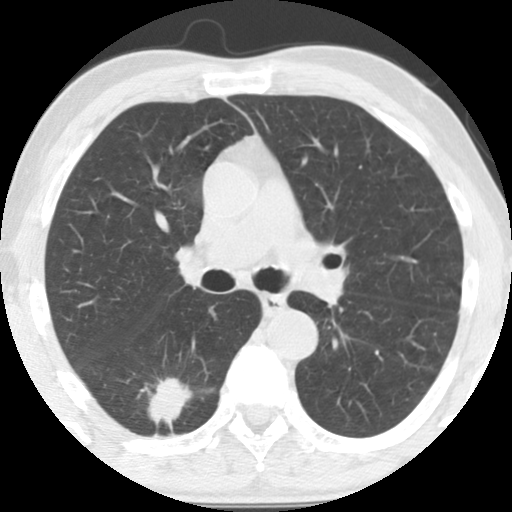
Low-dose screening chest CT, one axial slice. Position 87 of 135 along the scan axis. Reconstruction kernel STANDARD. 120 kVp. Lung window (W 1500 / L -600 HU). 2.5 mm slice thickness. 512 × 512 image matrix, field of view 300 × 300 mm.
Outlined on this slice (outlined manually by an expert reader):
- lesion 1 (tumor, lower lobe of right lung): bounding box [x1, y1, x2, y2] px = [149, 378, 190, 419]